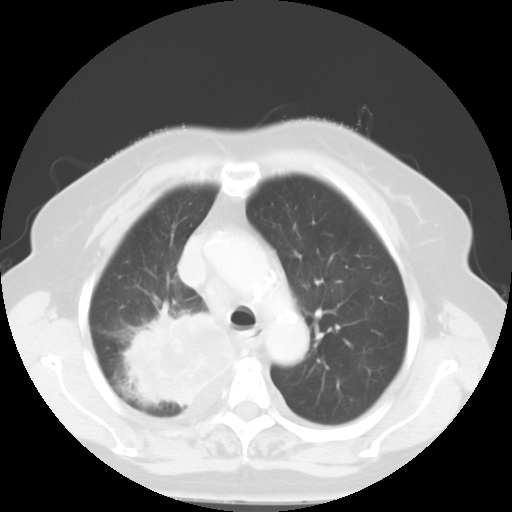
Chest CT, one axial slice; position 39 of 52 along the scan axis; lung window (W 1500 / L -600 HU); 5 mm slice thickness; 512 × 512 image matrix, field of view 333 × 333 mm. Patient: female, 81 years. From the clinical record (not read from this slice): clinical TNM (as recorded): T4 N3 M1b.
Structures marked on this image (rectangle marked by the reading radiologist):
- lung tumour (recorded histology: adenocarcinoma): bounding box (x1, y1, x2, y2) in pixels: (123, 300, 241, 406)